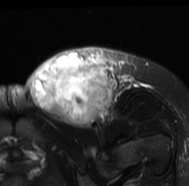
MRI of an extremity soft-tissue mass, one axial slice. Position 43 of 77 along the scan axis. T2-weighted fat-saturated. MR volume resampled by the dataset authors to the PET/CT grid (not the native acquisition matrix). 3.27 mm slice thickness. 189 × 186 image matrix, field of view 185 × 182 mm. Female patient. Case-level facts recorded for this patient, not image findings: histological type: leiomyosarcoma; grade: high; site of the primary tumour: groin.
Structures marked on this image (expert contour drawn on MRI and transferred to this co-registered scan by the dataset authors):
- gross tumour volume including surrounding oedema: bounding box [x1, y1, x2, y2] px = [26, 47, 141, 128]
- gross tumour volume (mass): [26, 52, 114, 126]